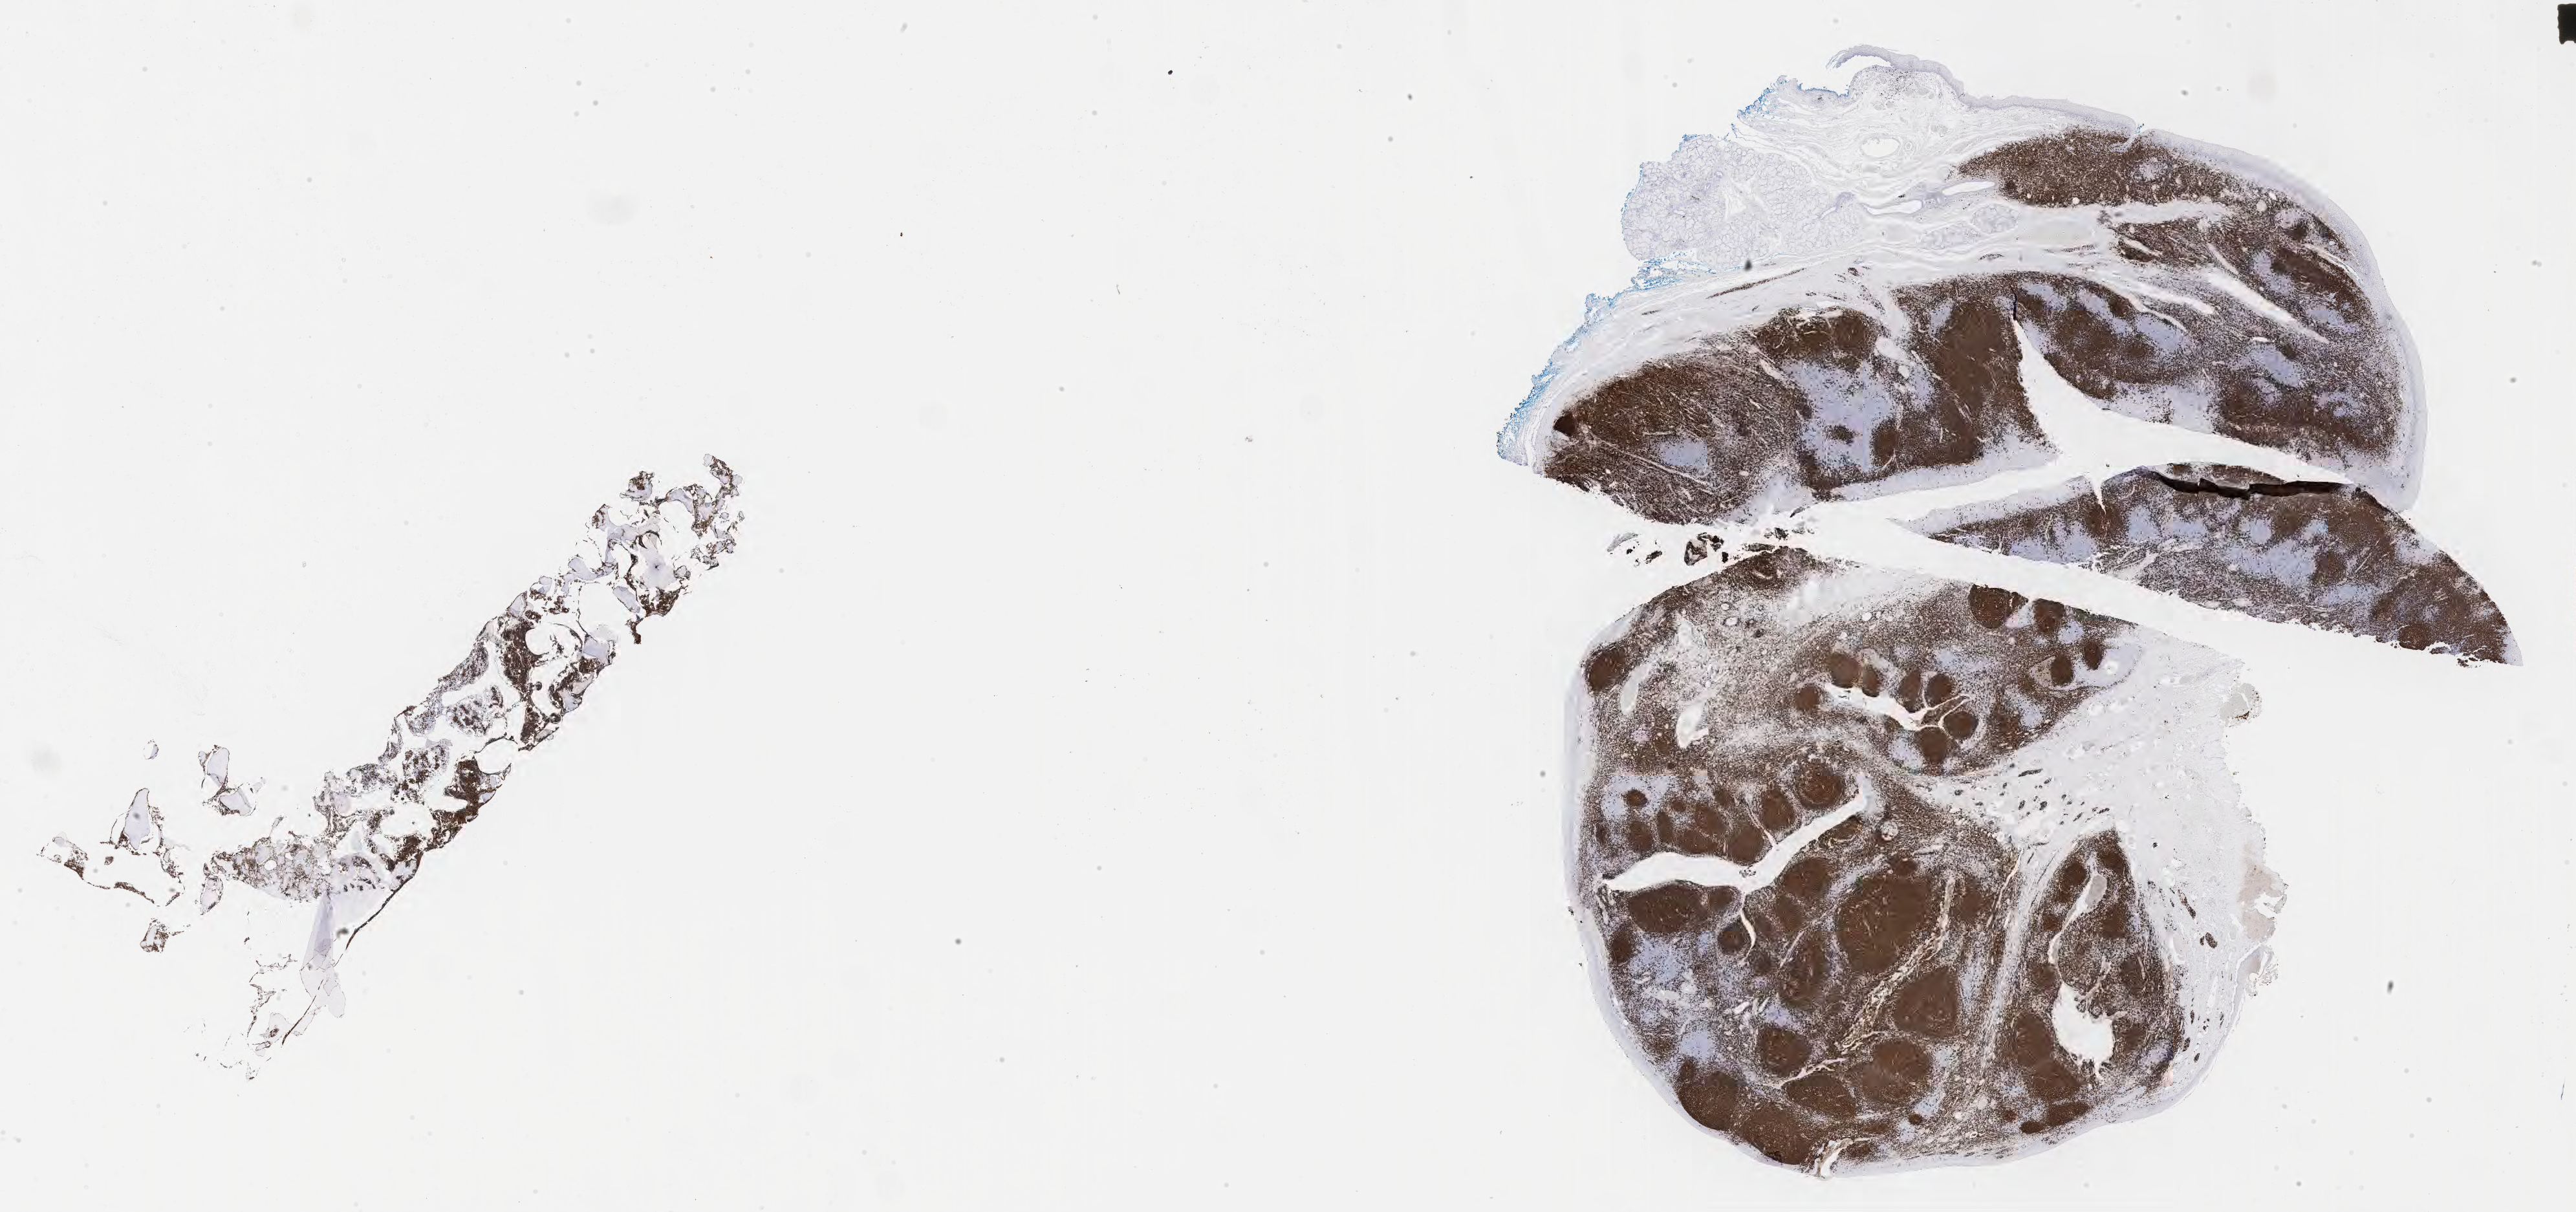
Immunohistochemistry (IHC) whole-slide image stained for CD20 — a low-resolution overview of the entire scanned area, about 32.2 x 15.2 mm, specimen: tumor tissue. Patient male; 13 years old.
Histologic diagnosis: Burkitt lymphoma, NOS.